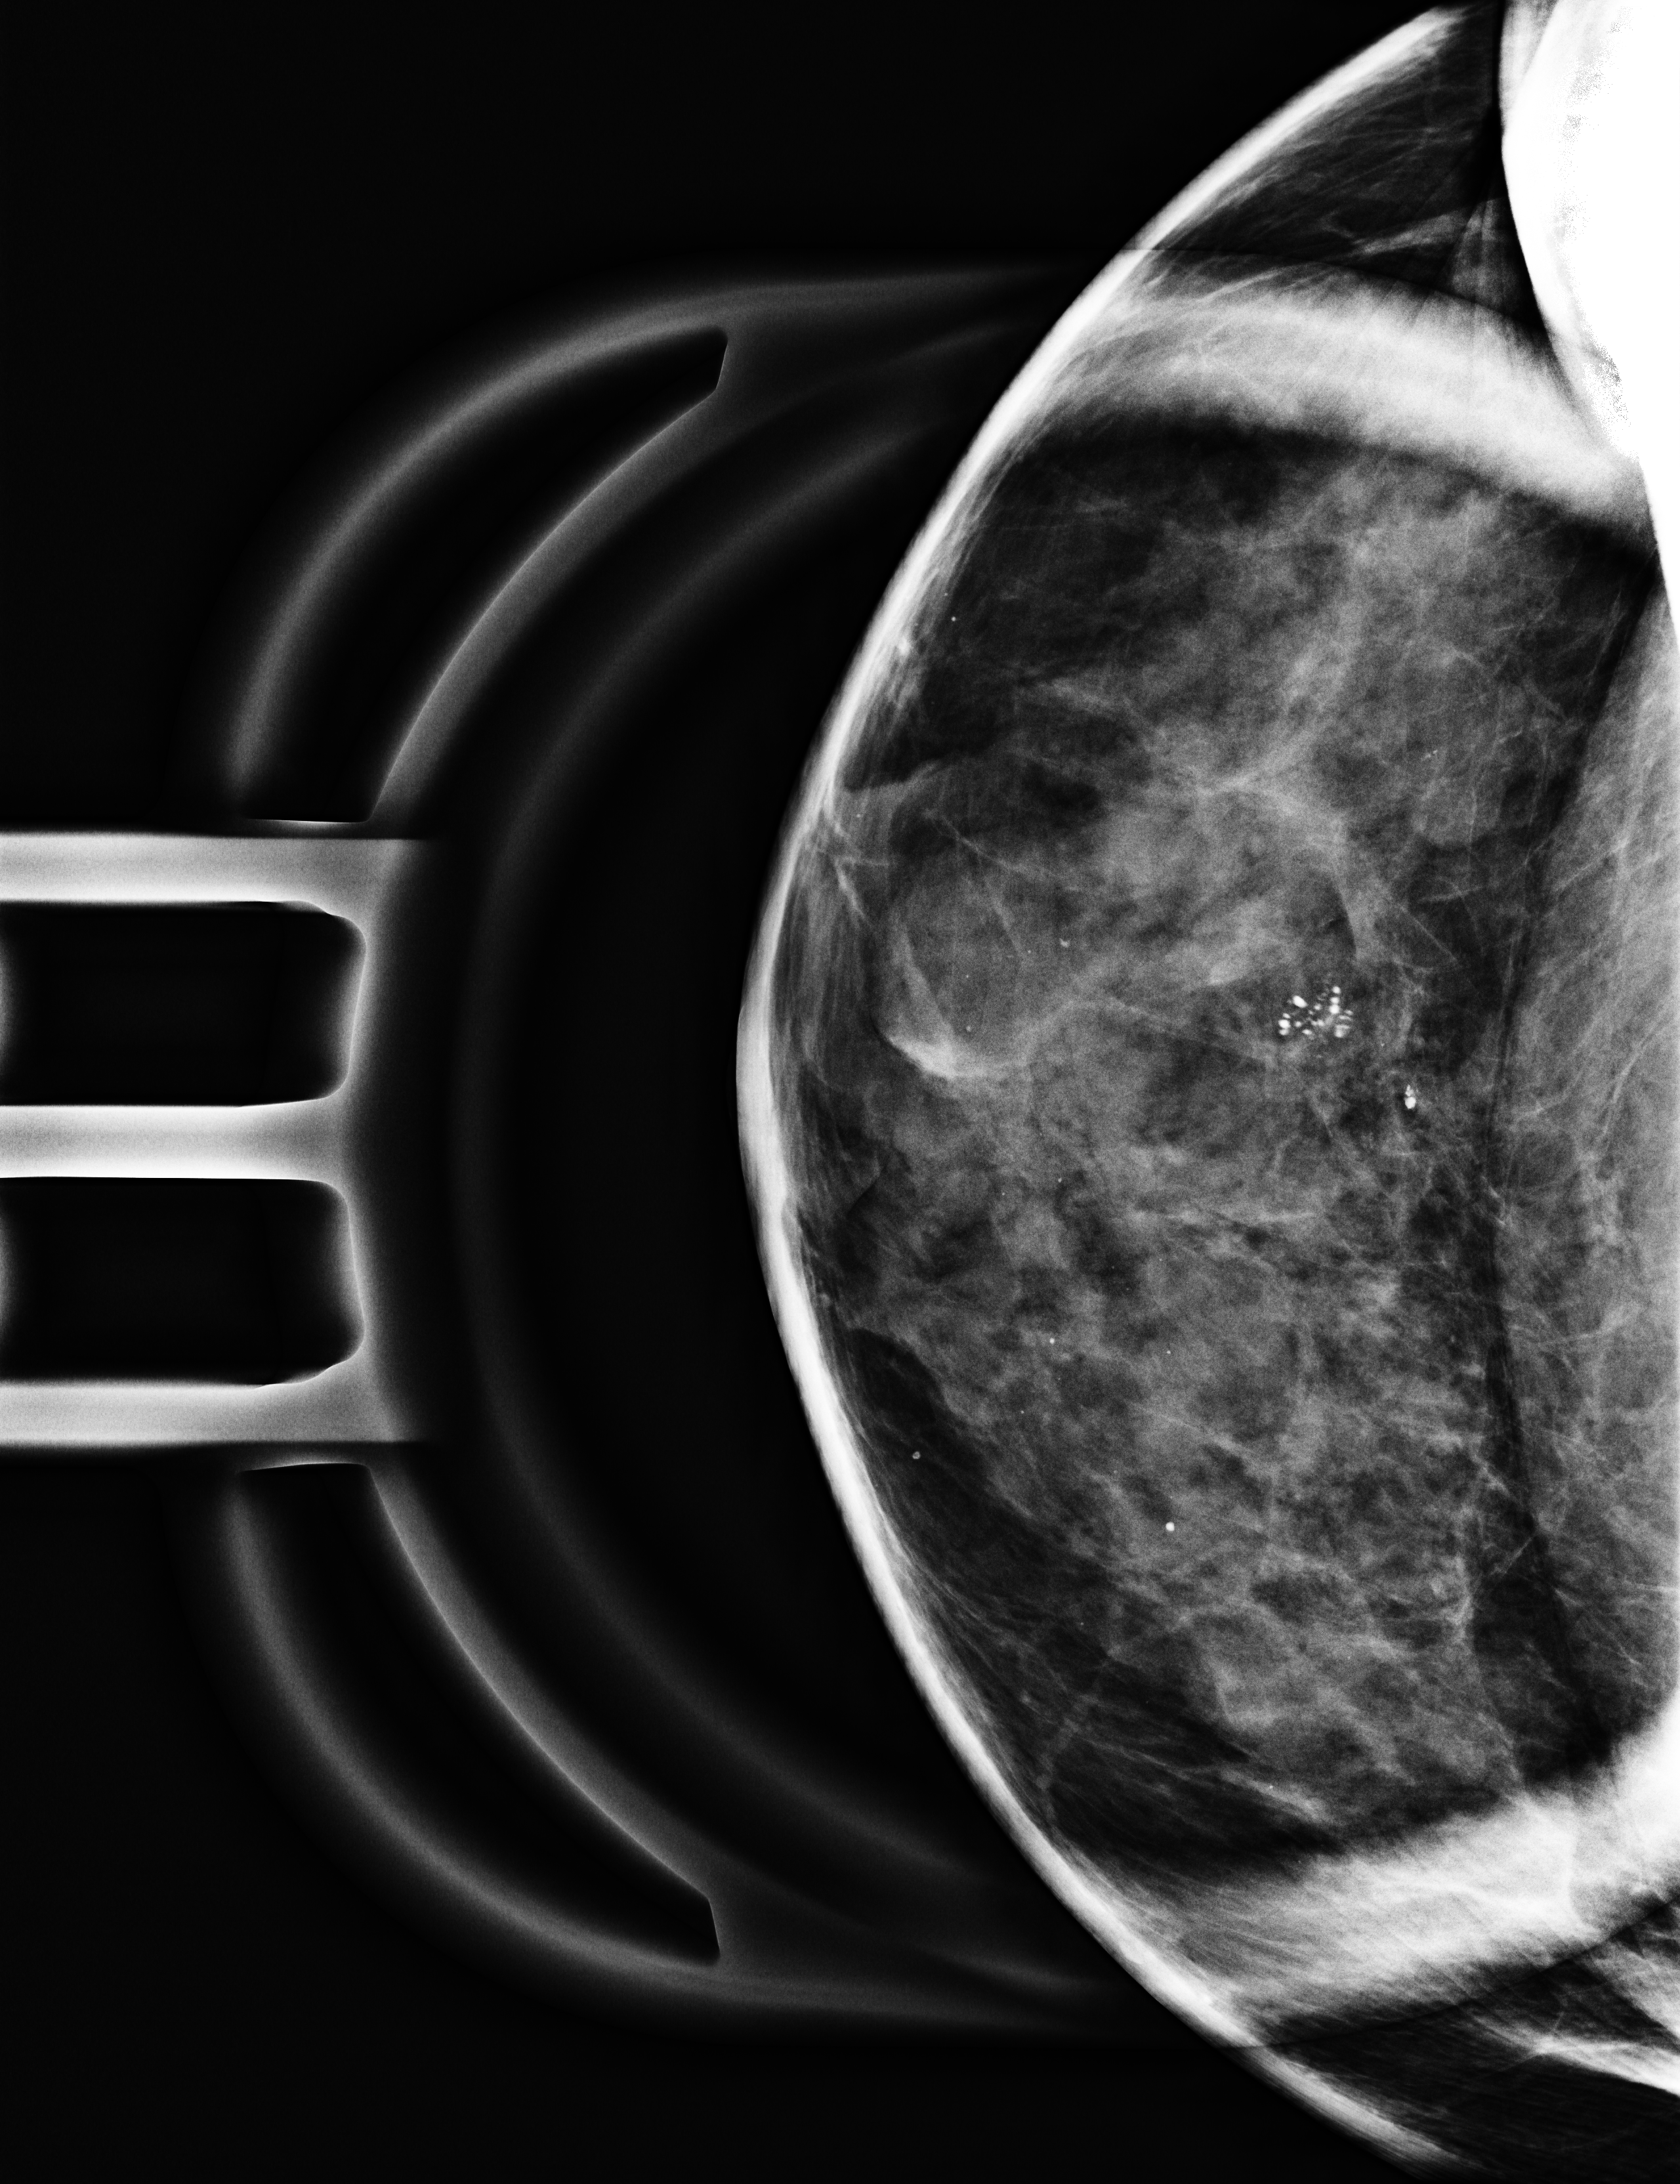
Additional work-up view; compressed breast thickness 41 mm. Patient aged 58 years (female).
Image type: full-field digital mammogram. Breast: right. Projection: cranio-caudal projection, magnification.